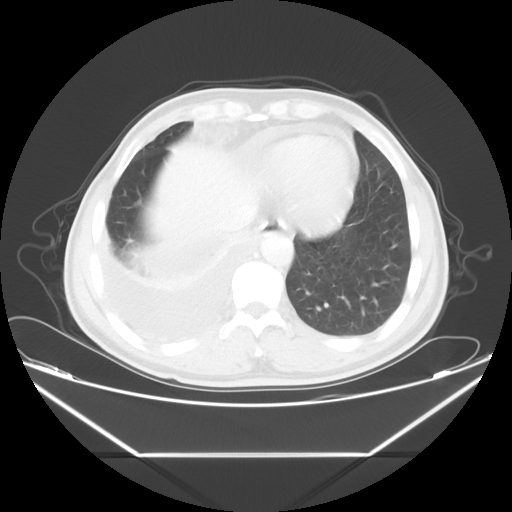
Chest CT, one axial slice. Position 12 of 56 along the scan axis. Reconstruction kernel STANDARD. 120 kVp. Lung window (W 1500 / L -600 HU). 512 × 512 image matrix. Male patient, age 57 years. Case-level facts recorded for this patient, not image findings: clinical TNM (as recorded): T2 N3 M1.
Outlined on this slice (rectangle marked by the reading radiologist):
- lung tumour (recorded histology: adenocarcinoma): bounding box (x1, y1, x2, y2) in pixels: (192, 121, 240, 150)